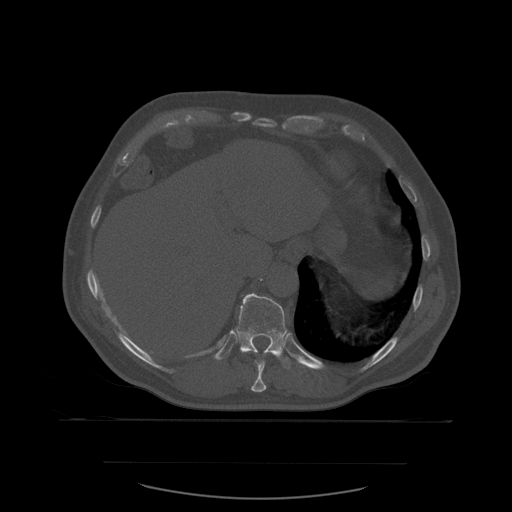
CT including the spine, one axial slice; position 305 of 590 along the scan axis; bone window (W 1800 / L 400 HU); 1.25 mm slice thickness; 512 × 512 image matrix. Patient age 71 years. From the clinical record (not read from this slice): primary cancer: lung.
Outlined on this slice (semi-automatic segmentation, software-assisted and operator-edited):
- T10 vertebra: bounding box (x1, y1, x2, y2) in pixels: (251, 361, 267, 393)
- T11 vertebra: (235, 294, 294, 369)